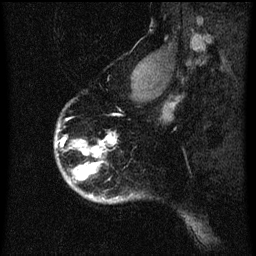
Breast MRI (dynamic contrast-enhanced), one sagittal slice; slice 51 of 60 in the series (ordered by position); dynamic contrast-enhanced series, image 2 of 3 at this slice position (ordered by acquisition); 1.5 T; TE 4.2 ms, TR 8 ms; 2 mm slice thickness; 256 × 256 image matrix. Patient: female, 56 years.
Outlined on this slice (semi-automatic segmentation, software-assisted and operator-edited):
- analysis volume of interest (the breast-tissue region the enhancement analysis was run in; not a lesion): box from (x=56, y=132) to (x=125, y=205) px
- tumour enhancement mask (voxels above the 70 % enhancement threshold inside the analysis volume of interest): (x=64, y=136)–(x=117, y=199)